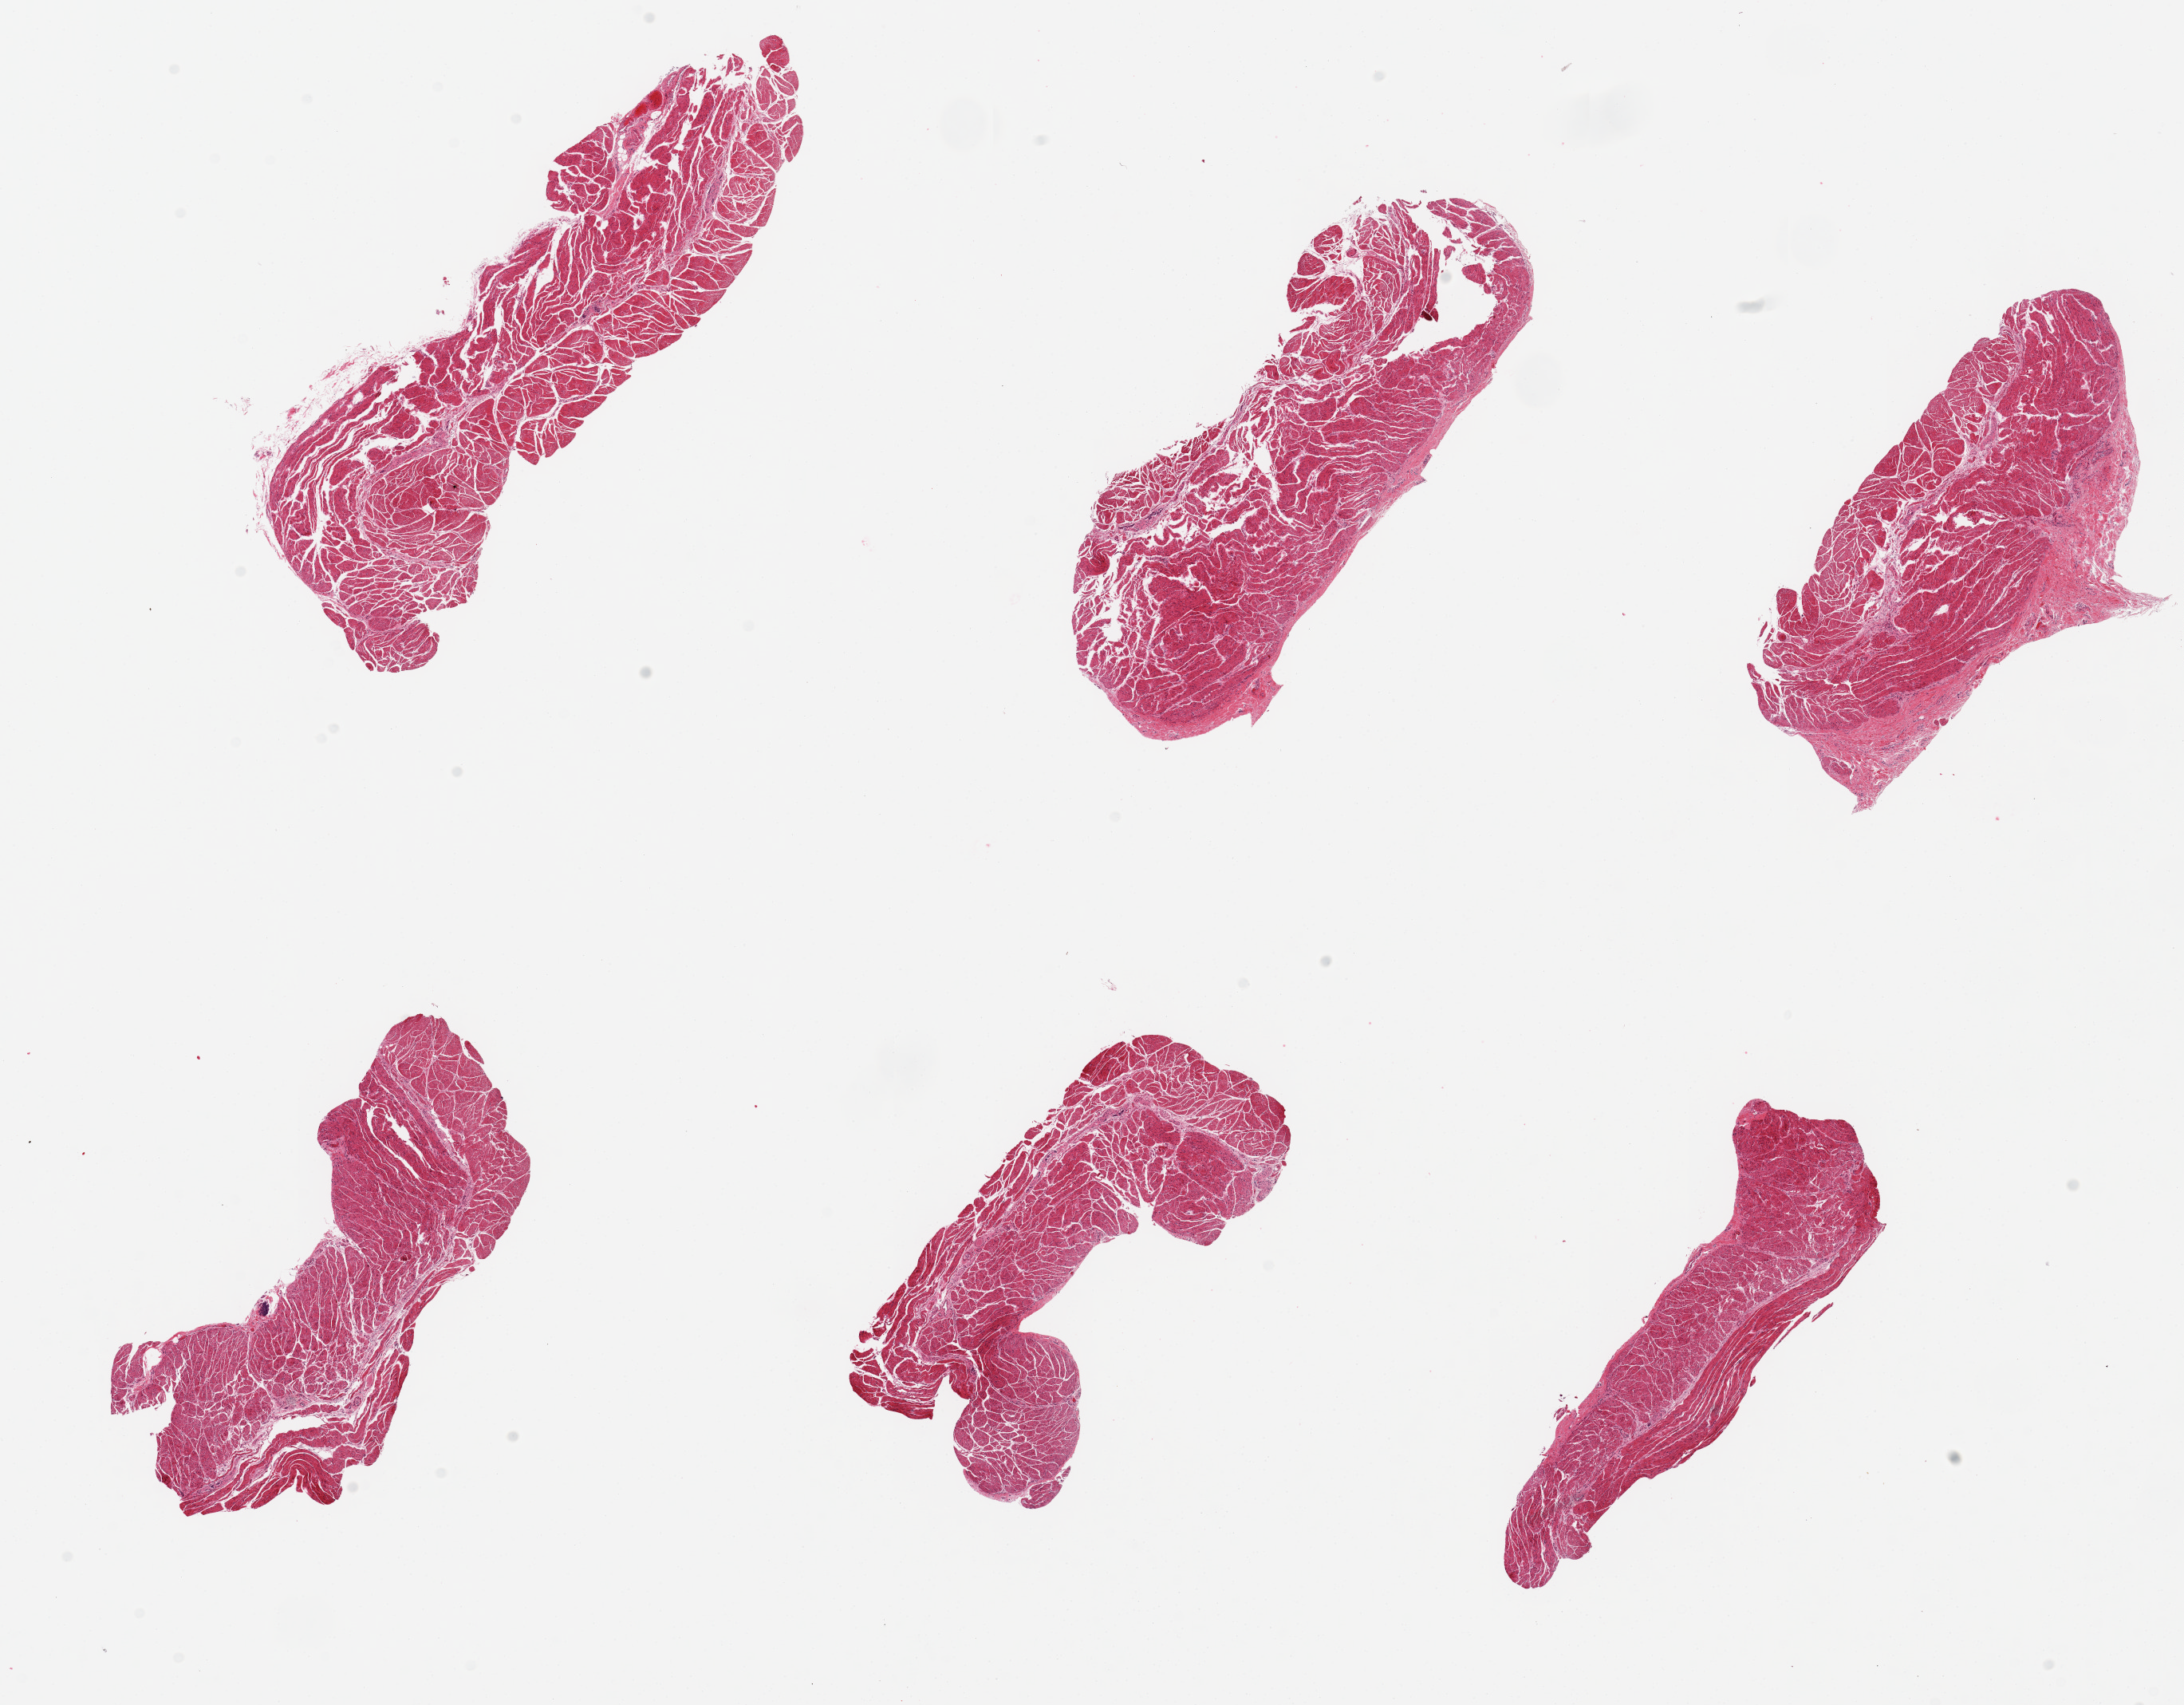
Hematoxylin and eosin (H&E) whole-slide image — shown as a low-resolution overview of the whole scanned area (about 21.7 x 16.9 mm, acquisition: 20x scan). PAXgene-fixed paraffin-embedded (PFPE) section. Section of esophageal muscle (target tissue). Donor tissue sample.
- reviewer comment on this tissue sample: 6 pieces; well trimmed